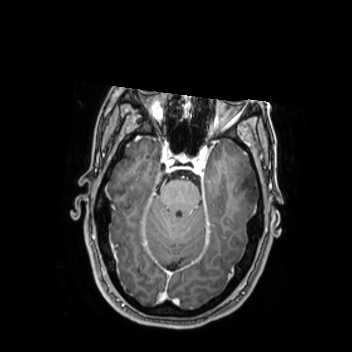
Brain MRI from a brain-tumour surgery series, one axial slice; position 171 of 350 along the scan axis; T1-weighted post-contrast; 0.9 mm slice thickness; 352 × 352 image matrix, field of view 280 × 280 mm. Case-level facts recorded for this patient, not image findings: histopathology: Oligodendroglioma; WHO grade: 2; IDH mutation: yes; tumour location: Left Middle Temporal Gyrus.
Annotated regions visible in this slice (expert manual segmentation):
- tumour: bounding box <228,164,256,215> (left, top, right, bottom; pixels)